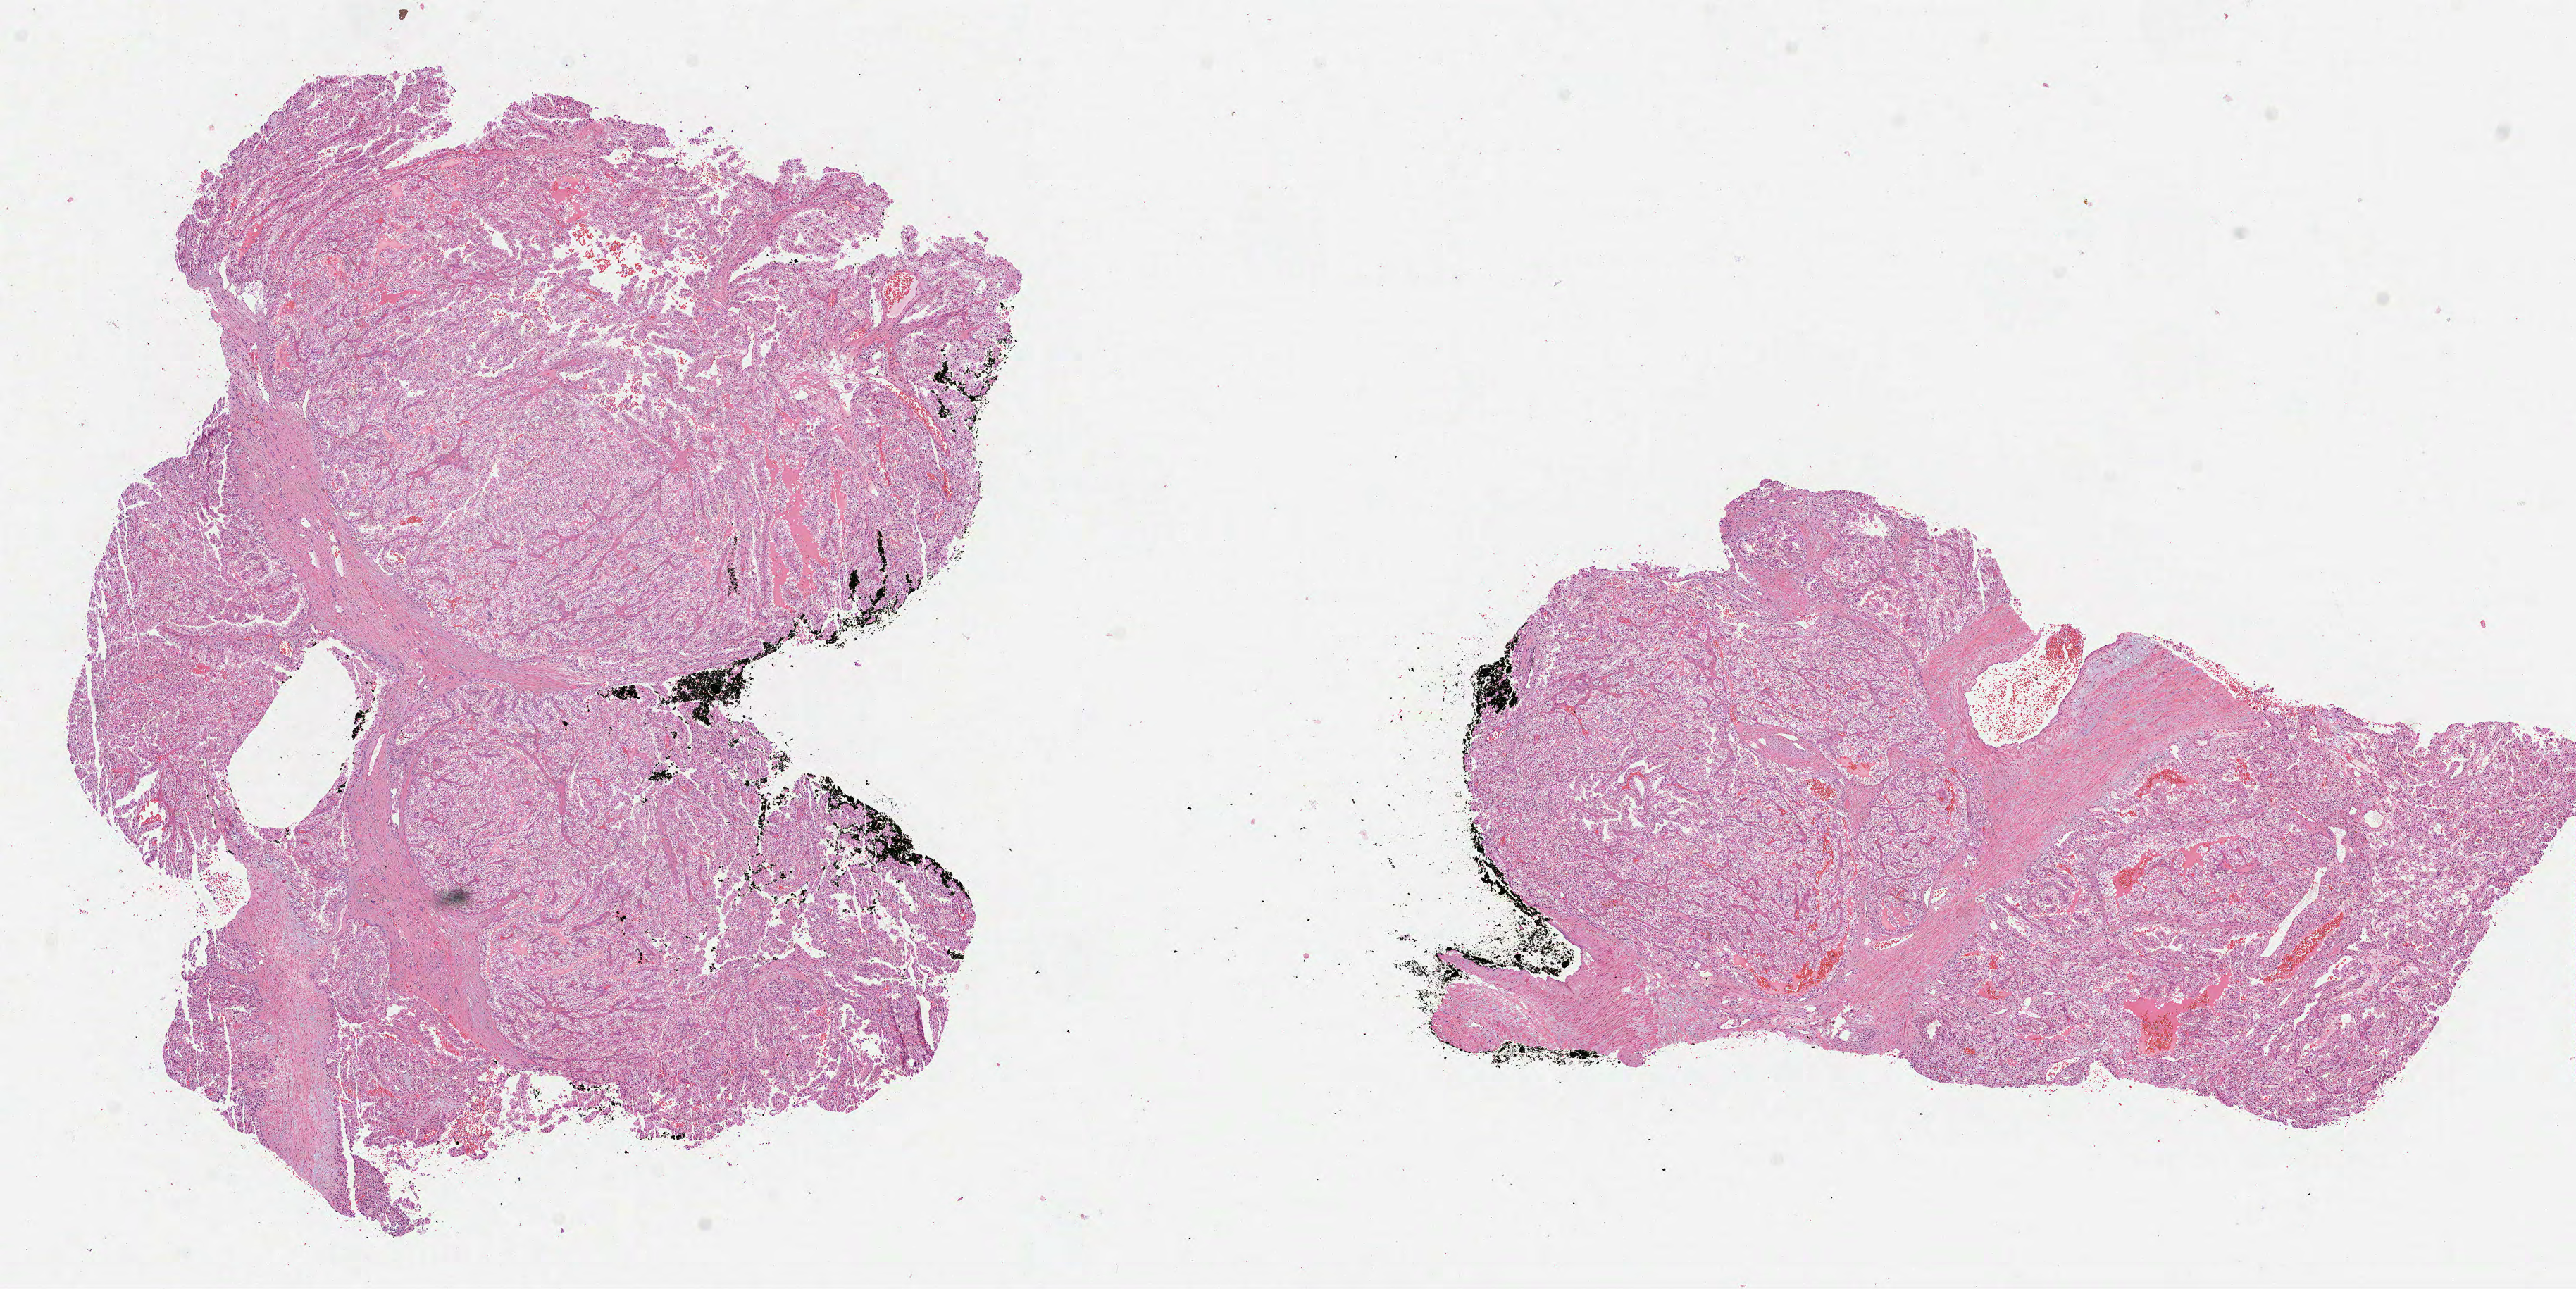
Hematoxylin and eosin (H&E) stained whole-slide image — low-resolution overview of the scanned area, about 14.7 x 7.4 mm (acquisition: 40x scan), formalin-fixed paraffin-embedded (FFPE) diagnostic section, sample: primary tumour, kidney. Patient: male, age at initial diagnosis 67 years. Histologic grade: G2 (moderately differentiated).
• AJCC pathologic stage: II
• histologic diagnosis: Clear cell adenocarcinoma, NOS